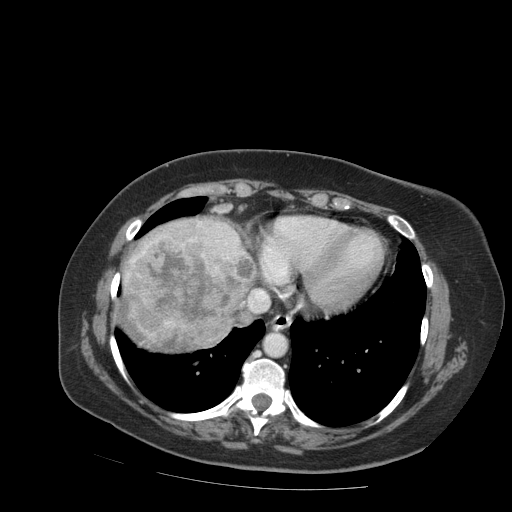
Contrast-enhanced abdominal CT (liver protocol), one axial slice; slice 81 of 99 in the series (ordered by position); reconstruction kernel STANDARD; 140 kVp; soft-tissue window (W 400 / L 40 HU); 2.5 mm slice thickness; 512 × 512 image matrix, field of view 400 × 400 mm. From the clinical record (not read from this slice): diagnosis: hepatocellular carcinoma (patient treated with transarterial chemoembolisation; whether this scan precedes or follows treatment is not stated here); TNM stage (as recorded): Stage-IVB; Child-Pugh class: A; tumour differentiation: moderately differentiated.
Outlined on this slice (semi-automatically segmented with operator editing):
- liver parenchyma outside the tumour (the mass and vessels are separate outlines, so this box may not span the whole liver): bounding box (x1, y1, x2, y2) in pixels: (114, 216, 252, 348)
- mass: (119, 240, 254, 353)
- liver vessels: (159, 221, 239, 259)